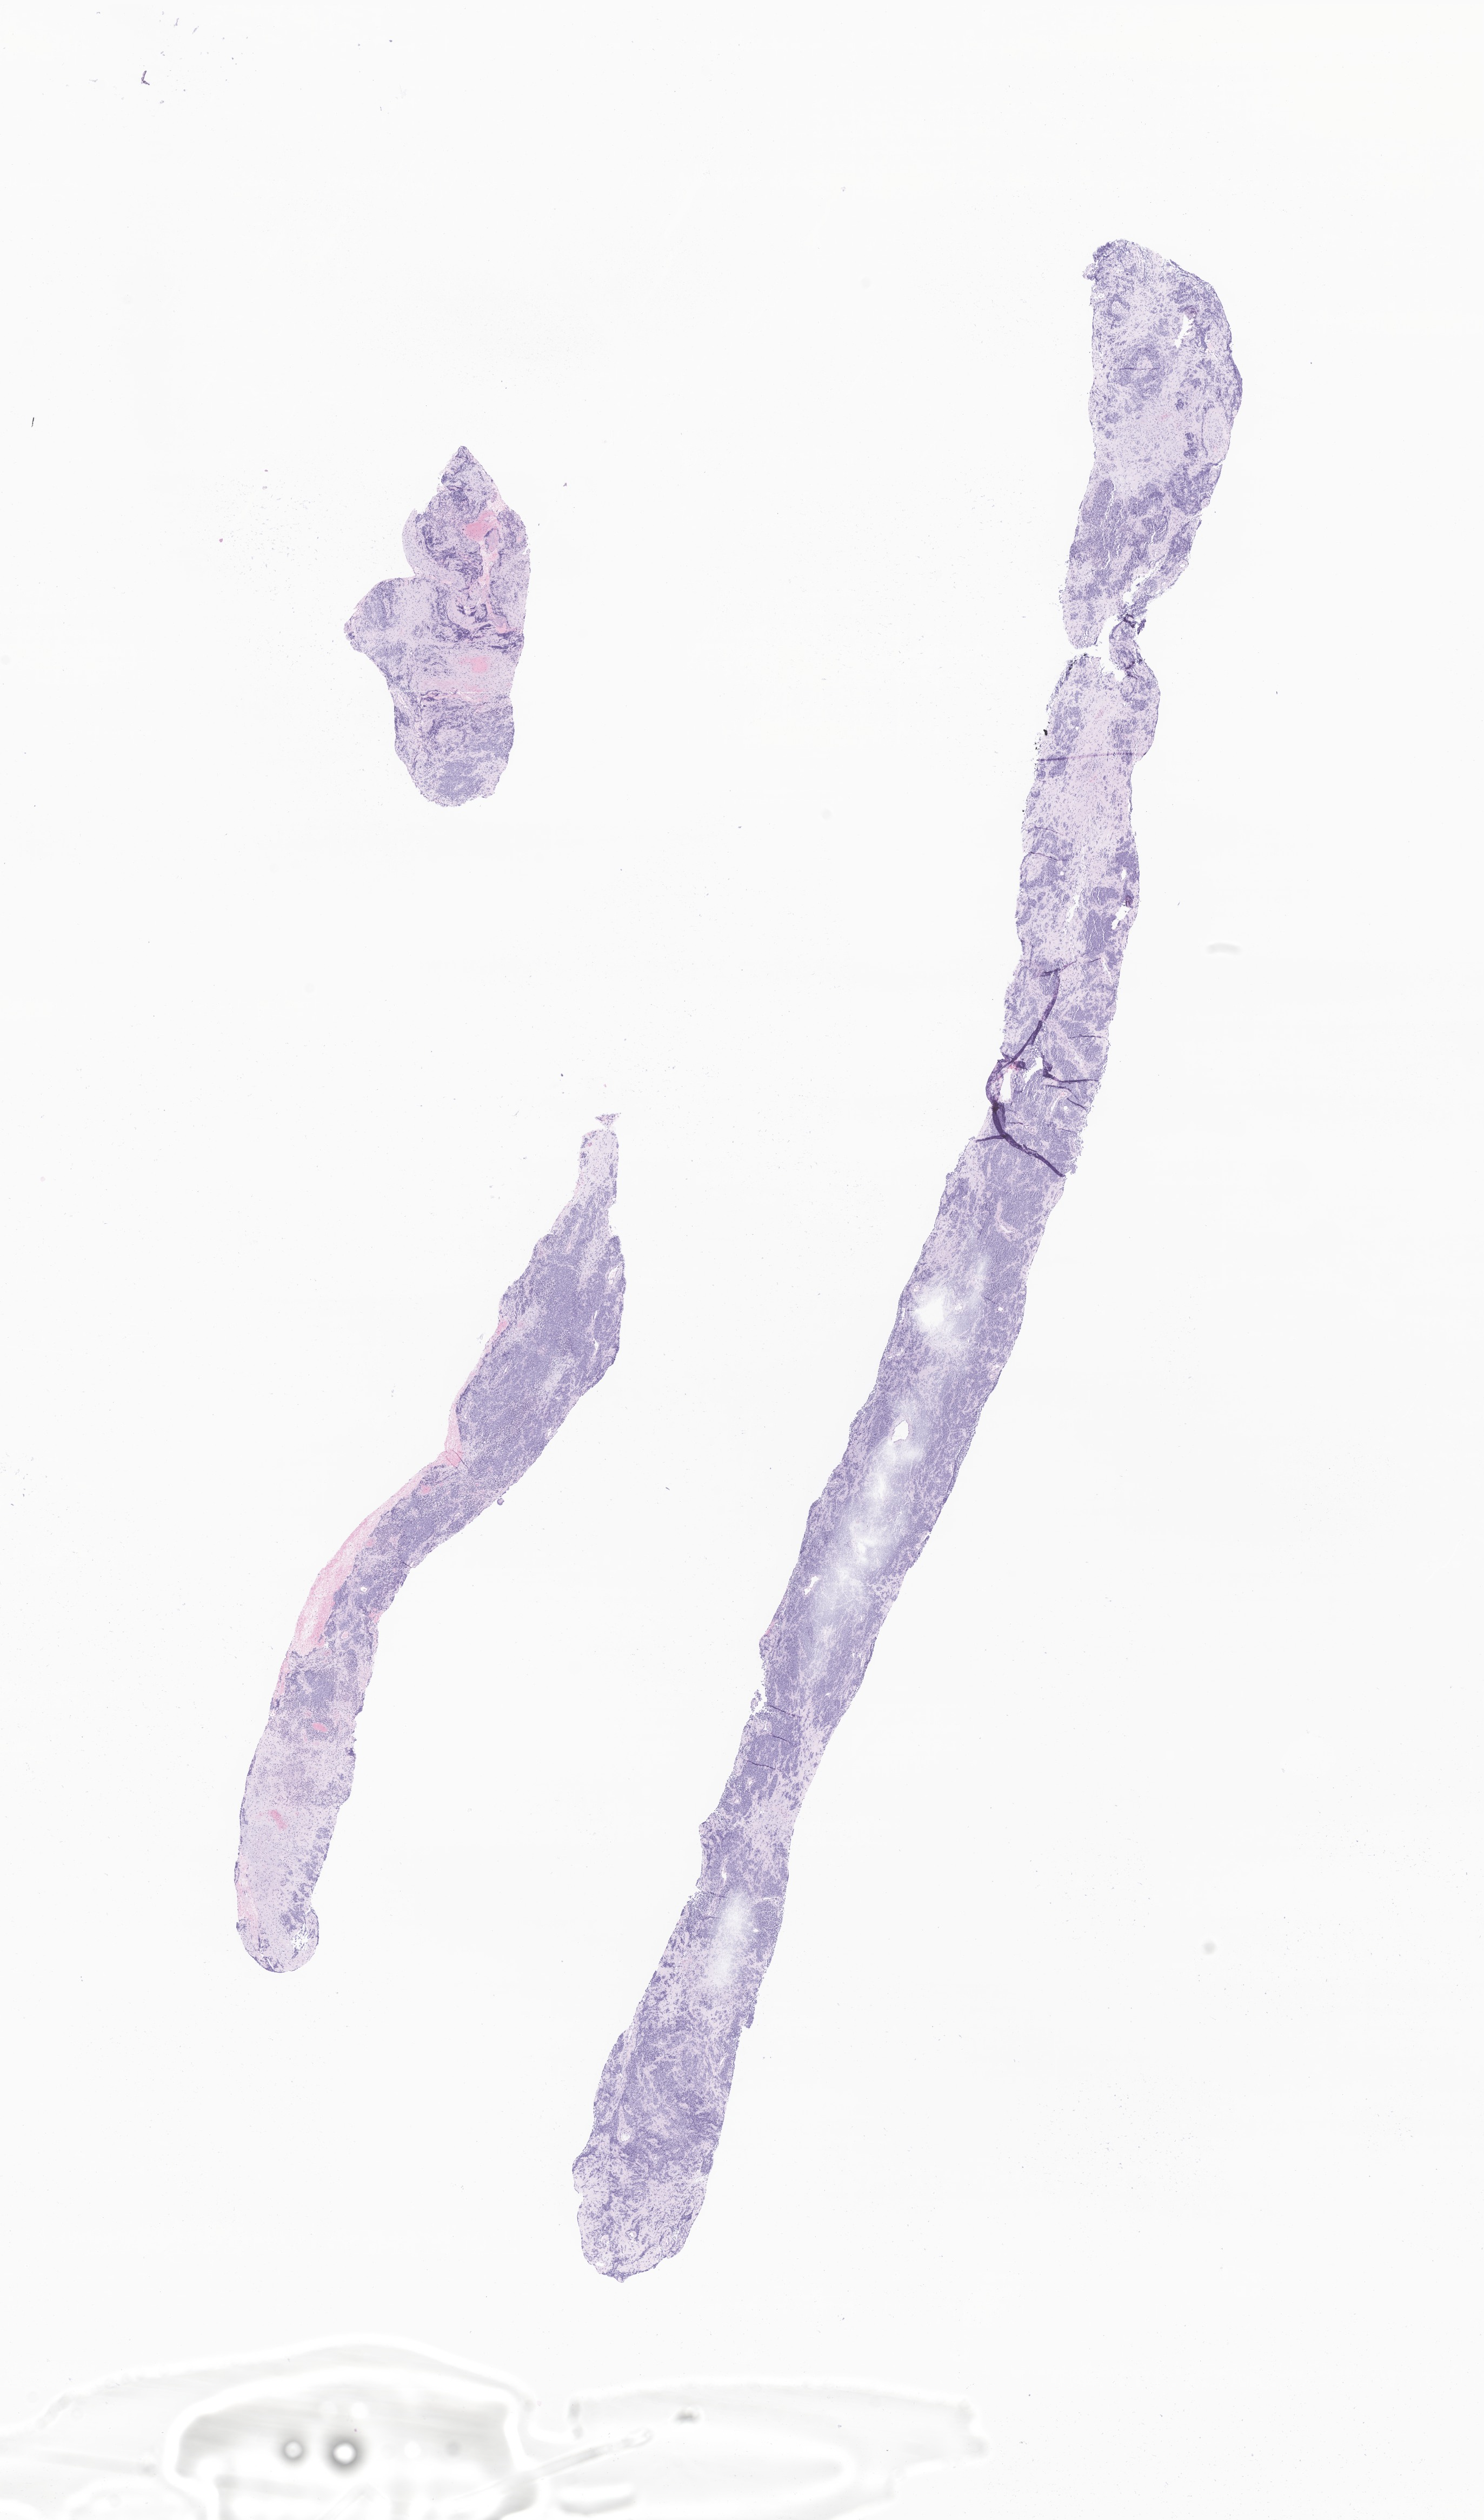
Whole-slide image, H&E stain of tumor tissue from the pancreas, shown as a low-resolution overview of the whole scanned area (about 11.6 x 19.7 mm); FFPE section. Patient: male, age 184 months (15 years 4 months).
Diagnosis: Sarcoma, NOS.